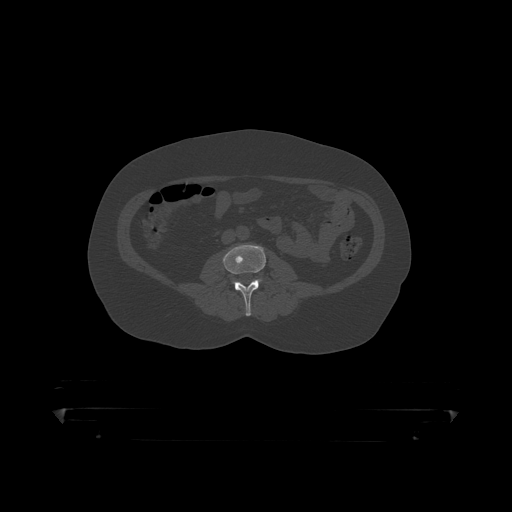
CT including the spine, one axial slice; slice 85 of 390 in the series (ordered by position); reconstruction kernel STANDARD; bone window (W 1800 / L 400 HU); 1.25 mm slice thickness; 512 × 512 image matrix, field of view 650 × 650 mm. Male patient, age 60 years. From the clinical record (not read from this slice): primary cancer: prostate.
Annotated regions visible in this slice (semi-automatic segmentation, software-assisted and operator-edited):
- L3 vertebra: bounding box (x1, y1, x2, y2) in pixels: (223, 245, 286, 317)